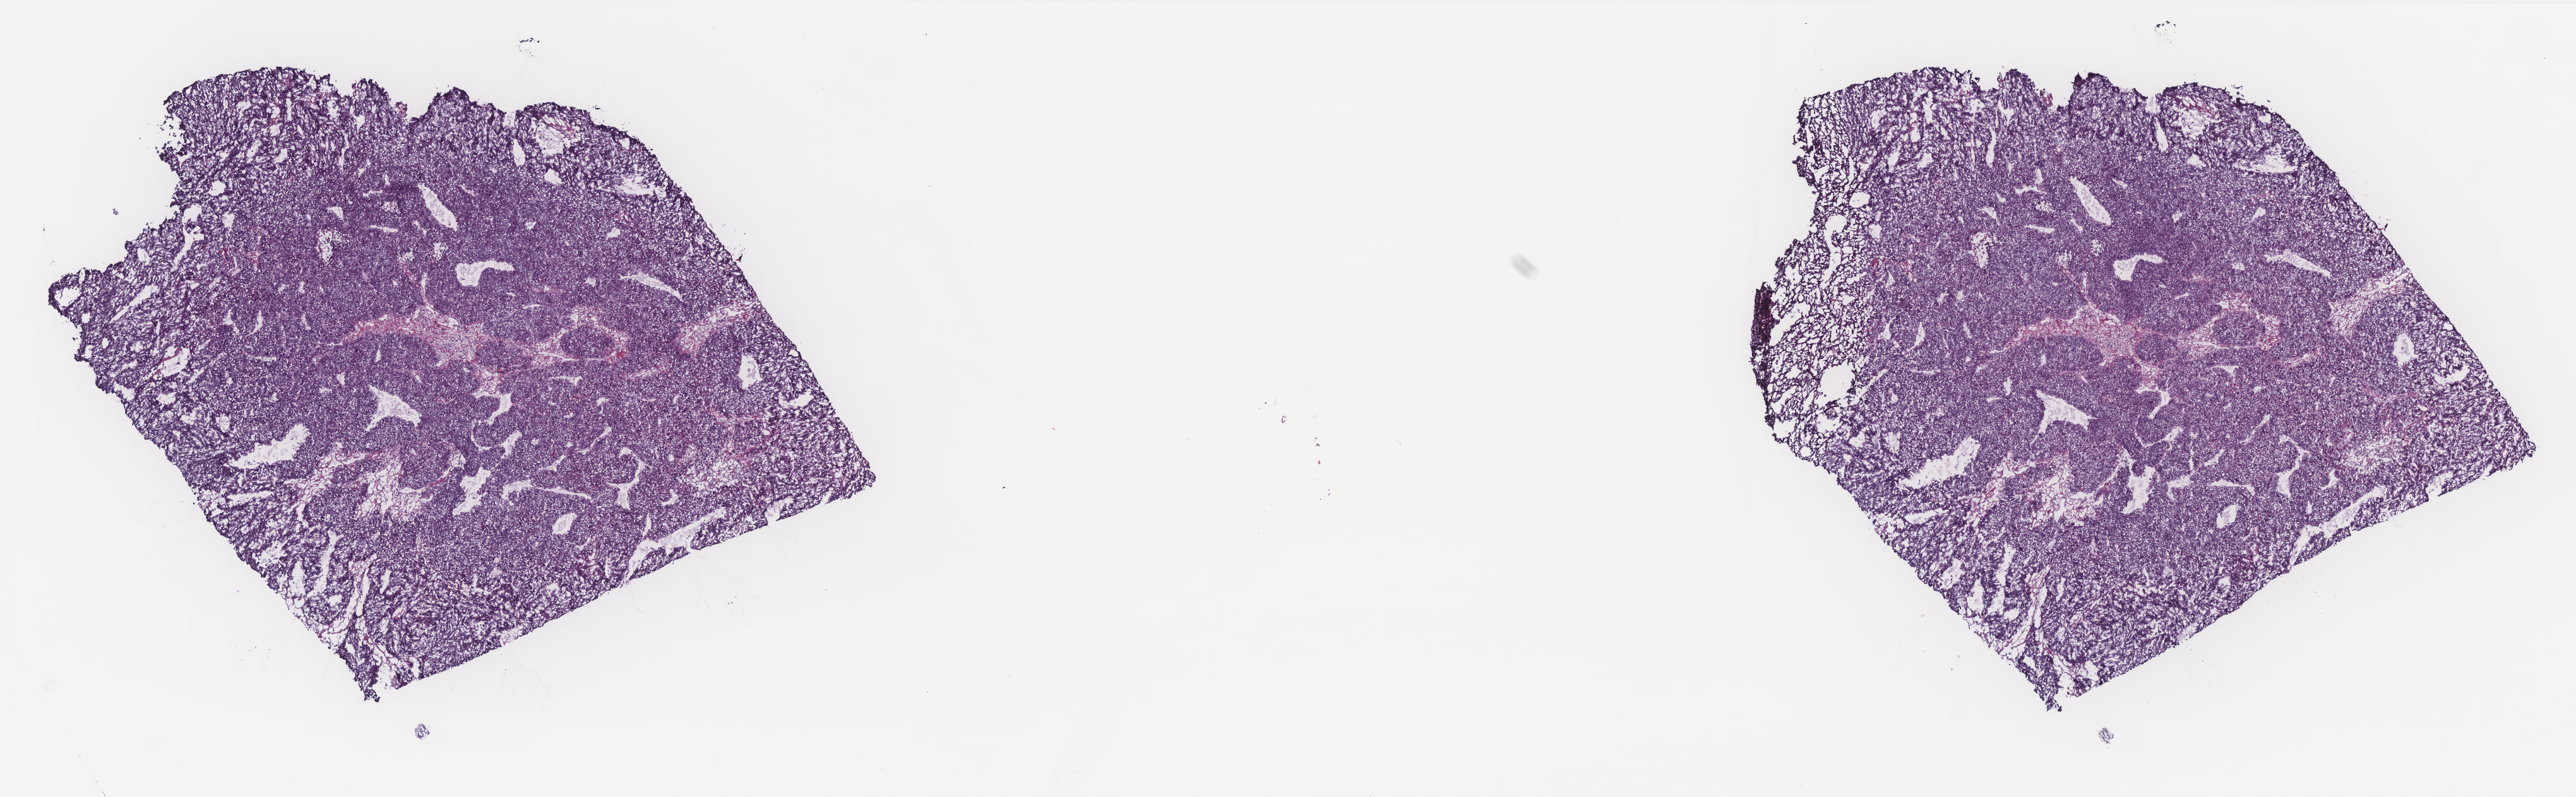
H&E-stained whole-slide image, a low-resolution overview of the entire scanned area, about 16.4 x 5.1 mm (acquisition: 40x scan); frozen section from the top of the tissue portion; liver, primary tumour sample. Female, age 71 years at initial diagnosis. Histologic grade: G2 (moderately differentiated). Pathologist review of this section (percent, as recorded): tumour cells 85%, tumour nuclei 85%, normal cells 0%, stromal cells 15%, necrosis 0%. Infiltration values recorded for this section: lymphocyte infiltration 5%, monocyte infiltration 0%, neutrophil infiltration 0%.
AJCC pathologic stage: IIIC. Diagnosis: Hepatocellular carcinoma, NOS.